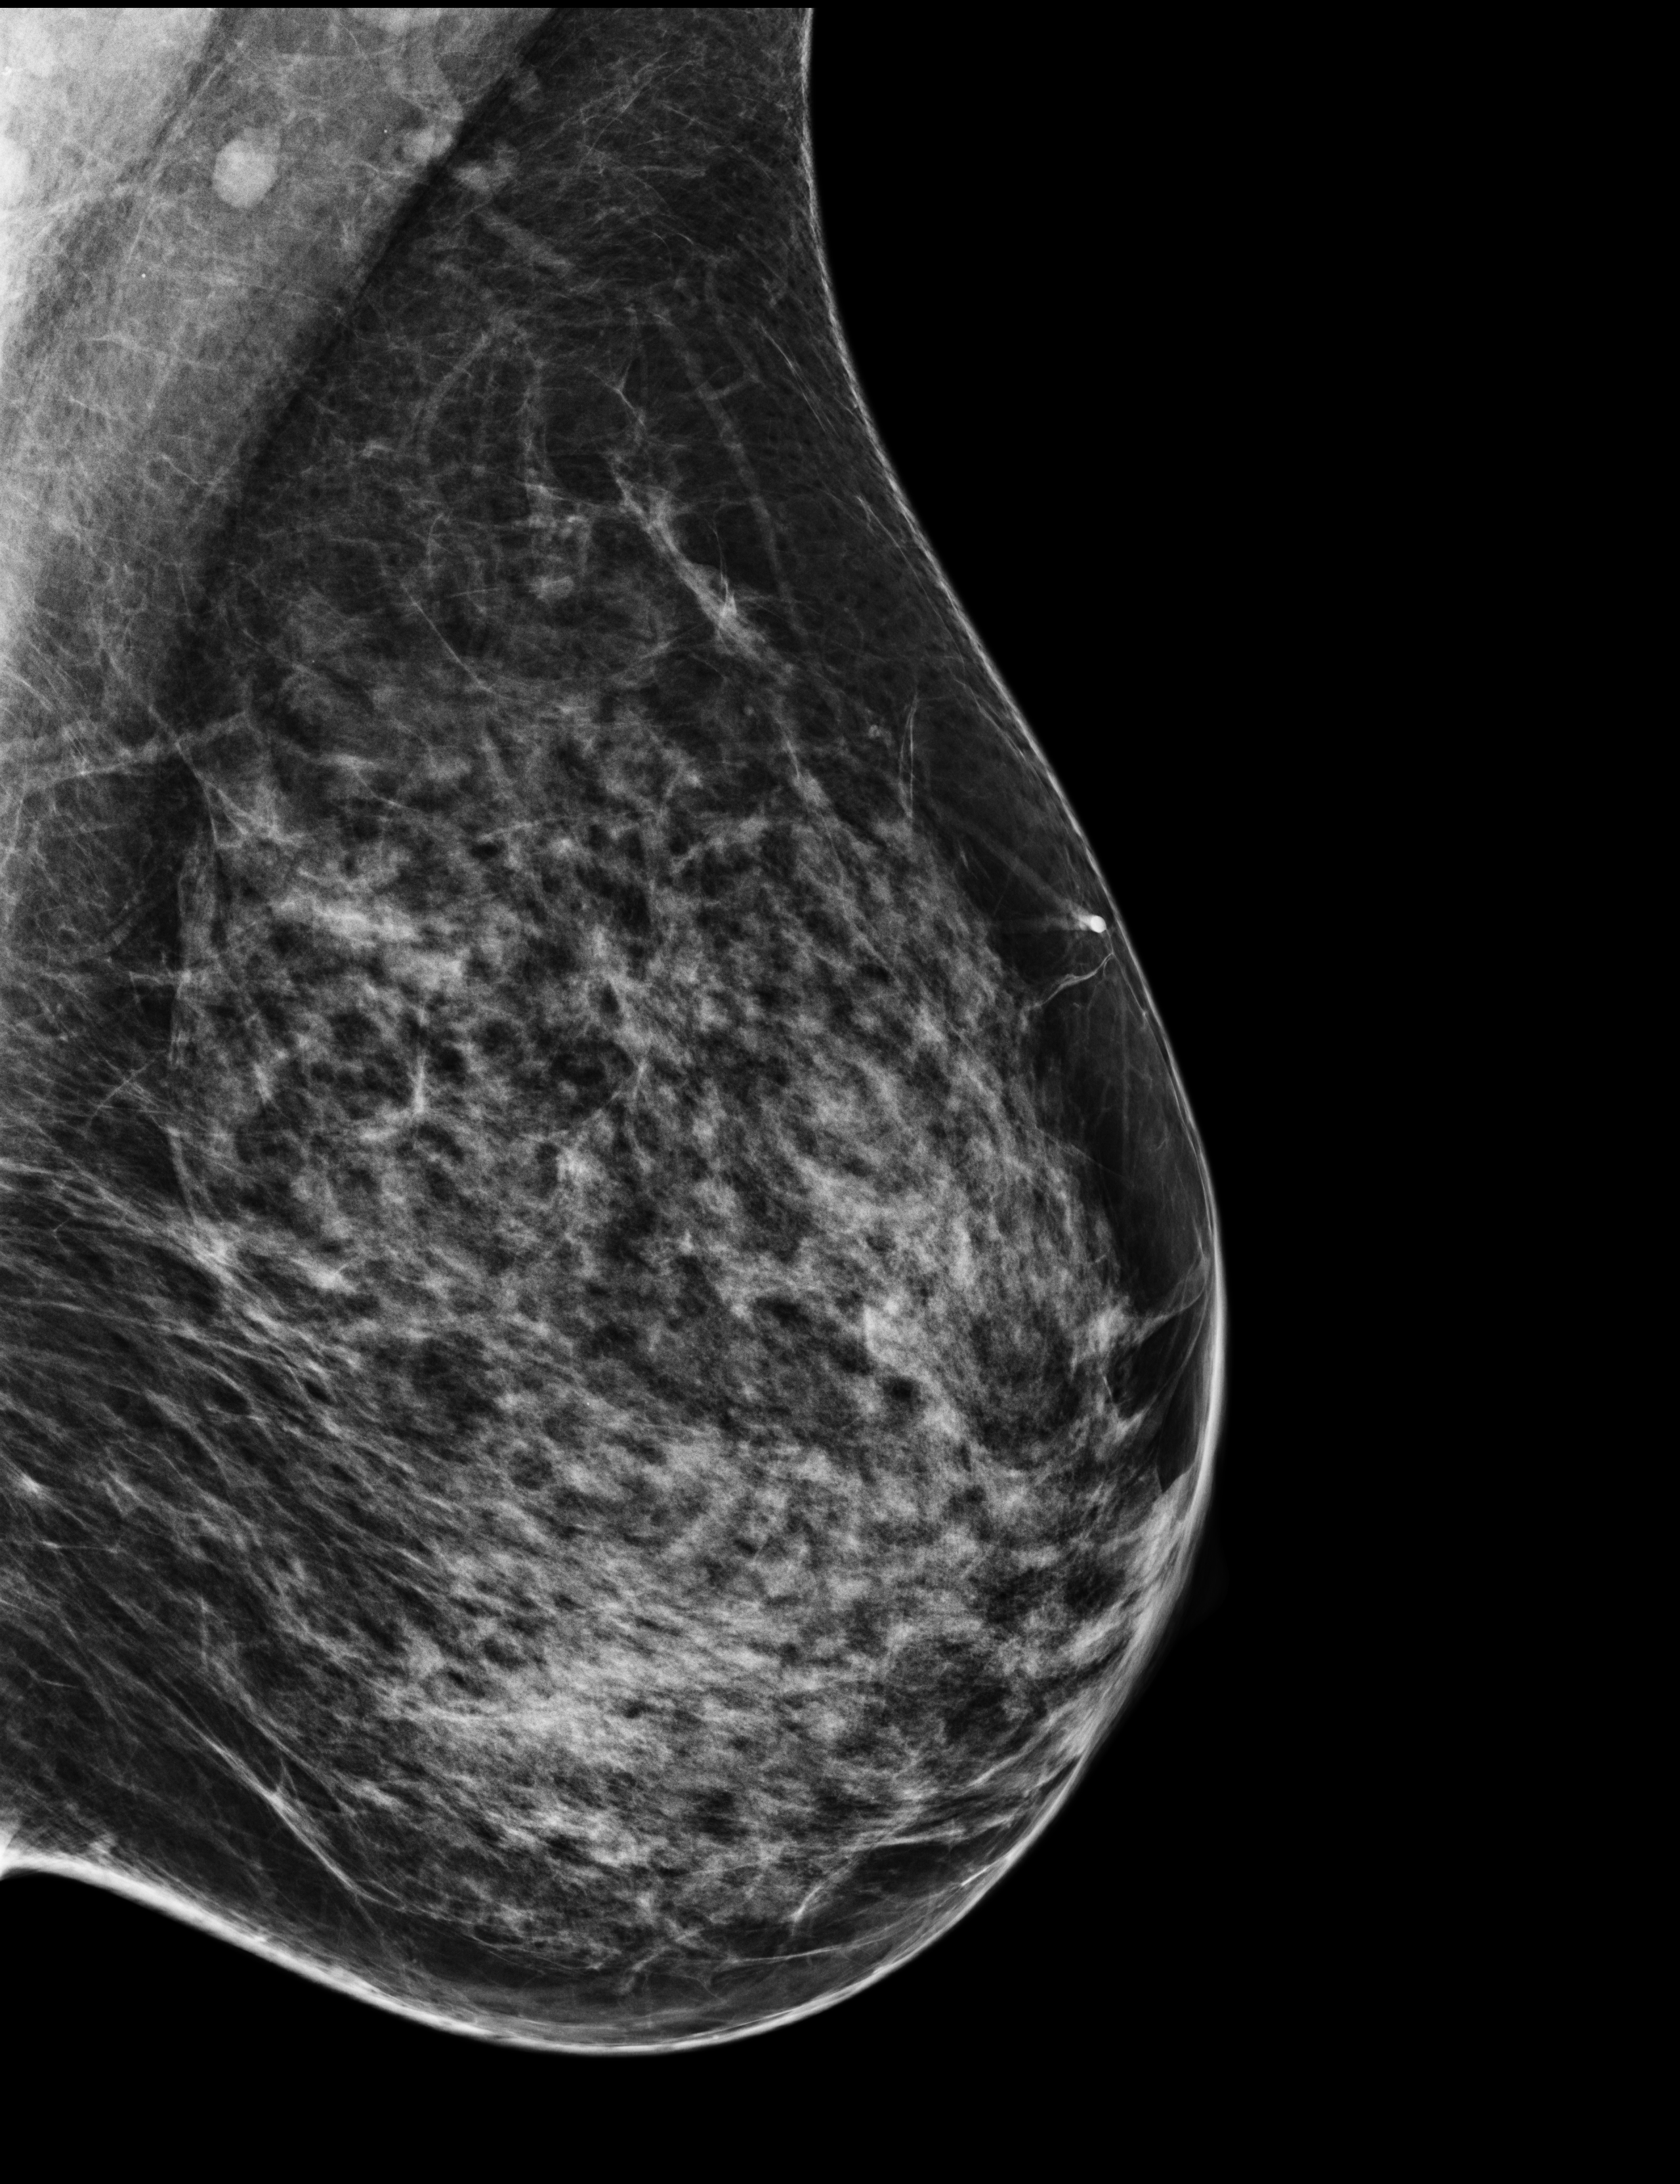
Digital mammogram (FFDM); left breast; mediolateral oblique (MLO) view; screening examination; compressed breast thickness 74 mm; system: Selenia Dimensions. Patient: female, 58 years.
BI-RADS breast density category at the screening exam (both breasts, scale 1–4): 3. Final BI-RADS category for the screening round (tomosynthesis exam, both breasts): category 1. Recall: no recall after this screen.